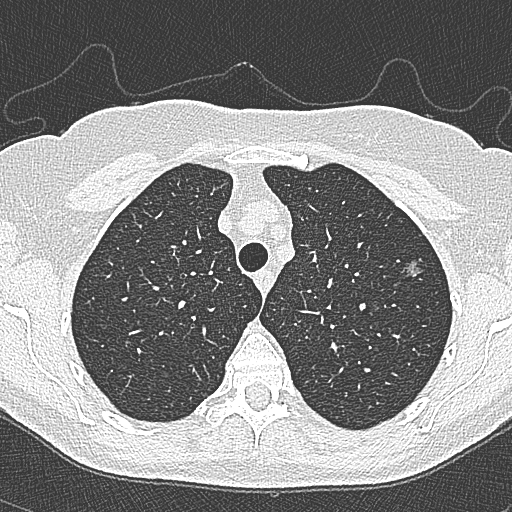
Axial slice from a low-dose chest CT screening exam, second annual screen, lung window (W 1500 / L -600 HU). Female, age 65 years at enrolment.
Expert-annotated lung lesion, bounding box <395,251,432,287> (left, top, right, bottom; pixels). The screening reader recorded 4 non-calcified nodules or masses ≥4 mm on this exam; which of them this box marks is not recorded. Participant outcome: lung cancer diagnosed 54 days after this screen — bronchiolo-alveolar carcinoma, non-mucinous, left upper lobe, stage IA (AJCC 6th edition), 10 mm at pathology.